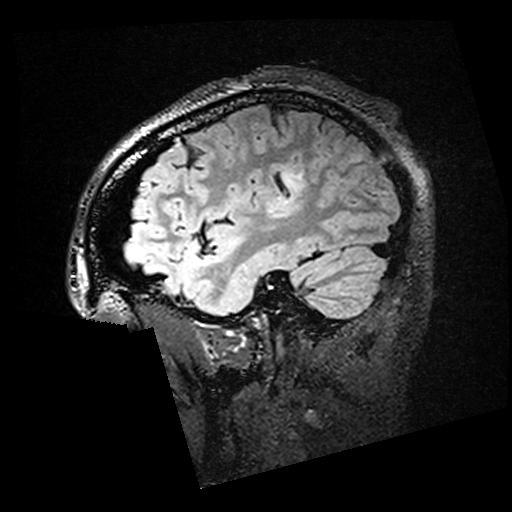
Brain MRI from a brain-tumour surgery series, one sagittal slice; position 44 of 176 along the scan axis; T2 FLAIR; 1 mm slice thickness; 512 × 512 image matrix. Case-level facts recorded for this patient, not image findings: histopathology: Oligodendroglioma; WHO grade: 2.
Annotated regions visible in this slice (outlined manually by an expert reader):
- residual tumour: bounding box (x1, y1, x2, y2) in pixels: (282, 173, 305, 190)